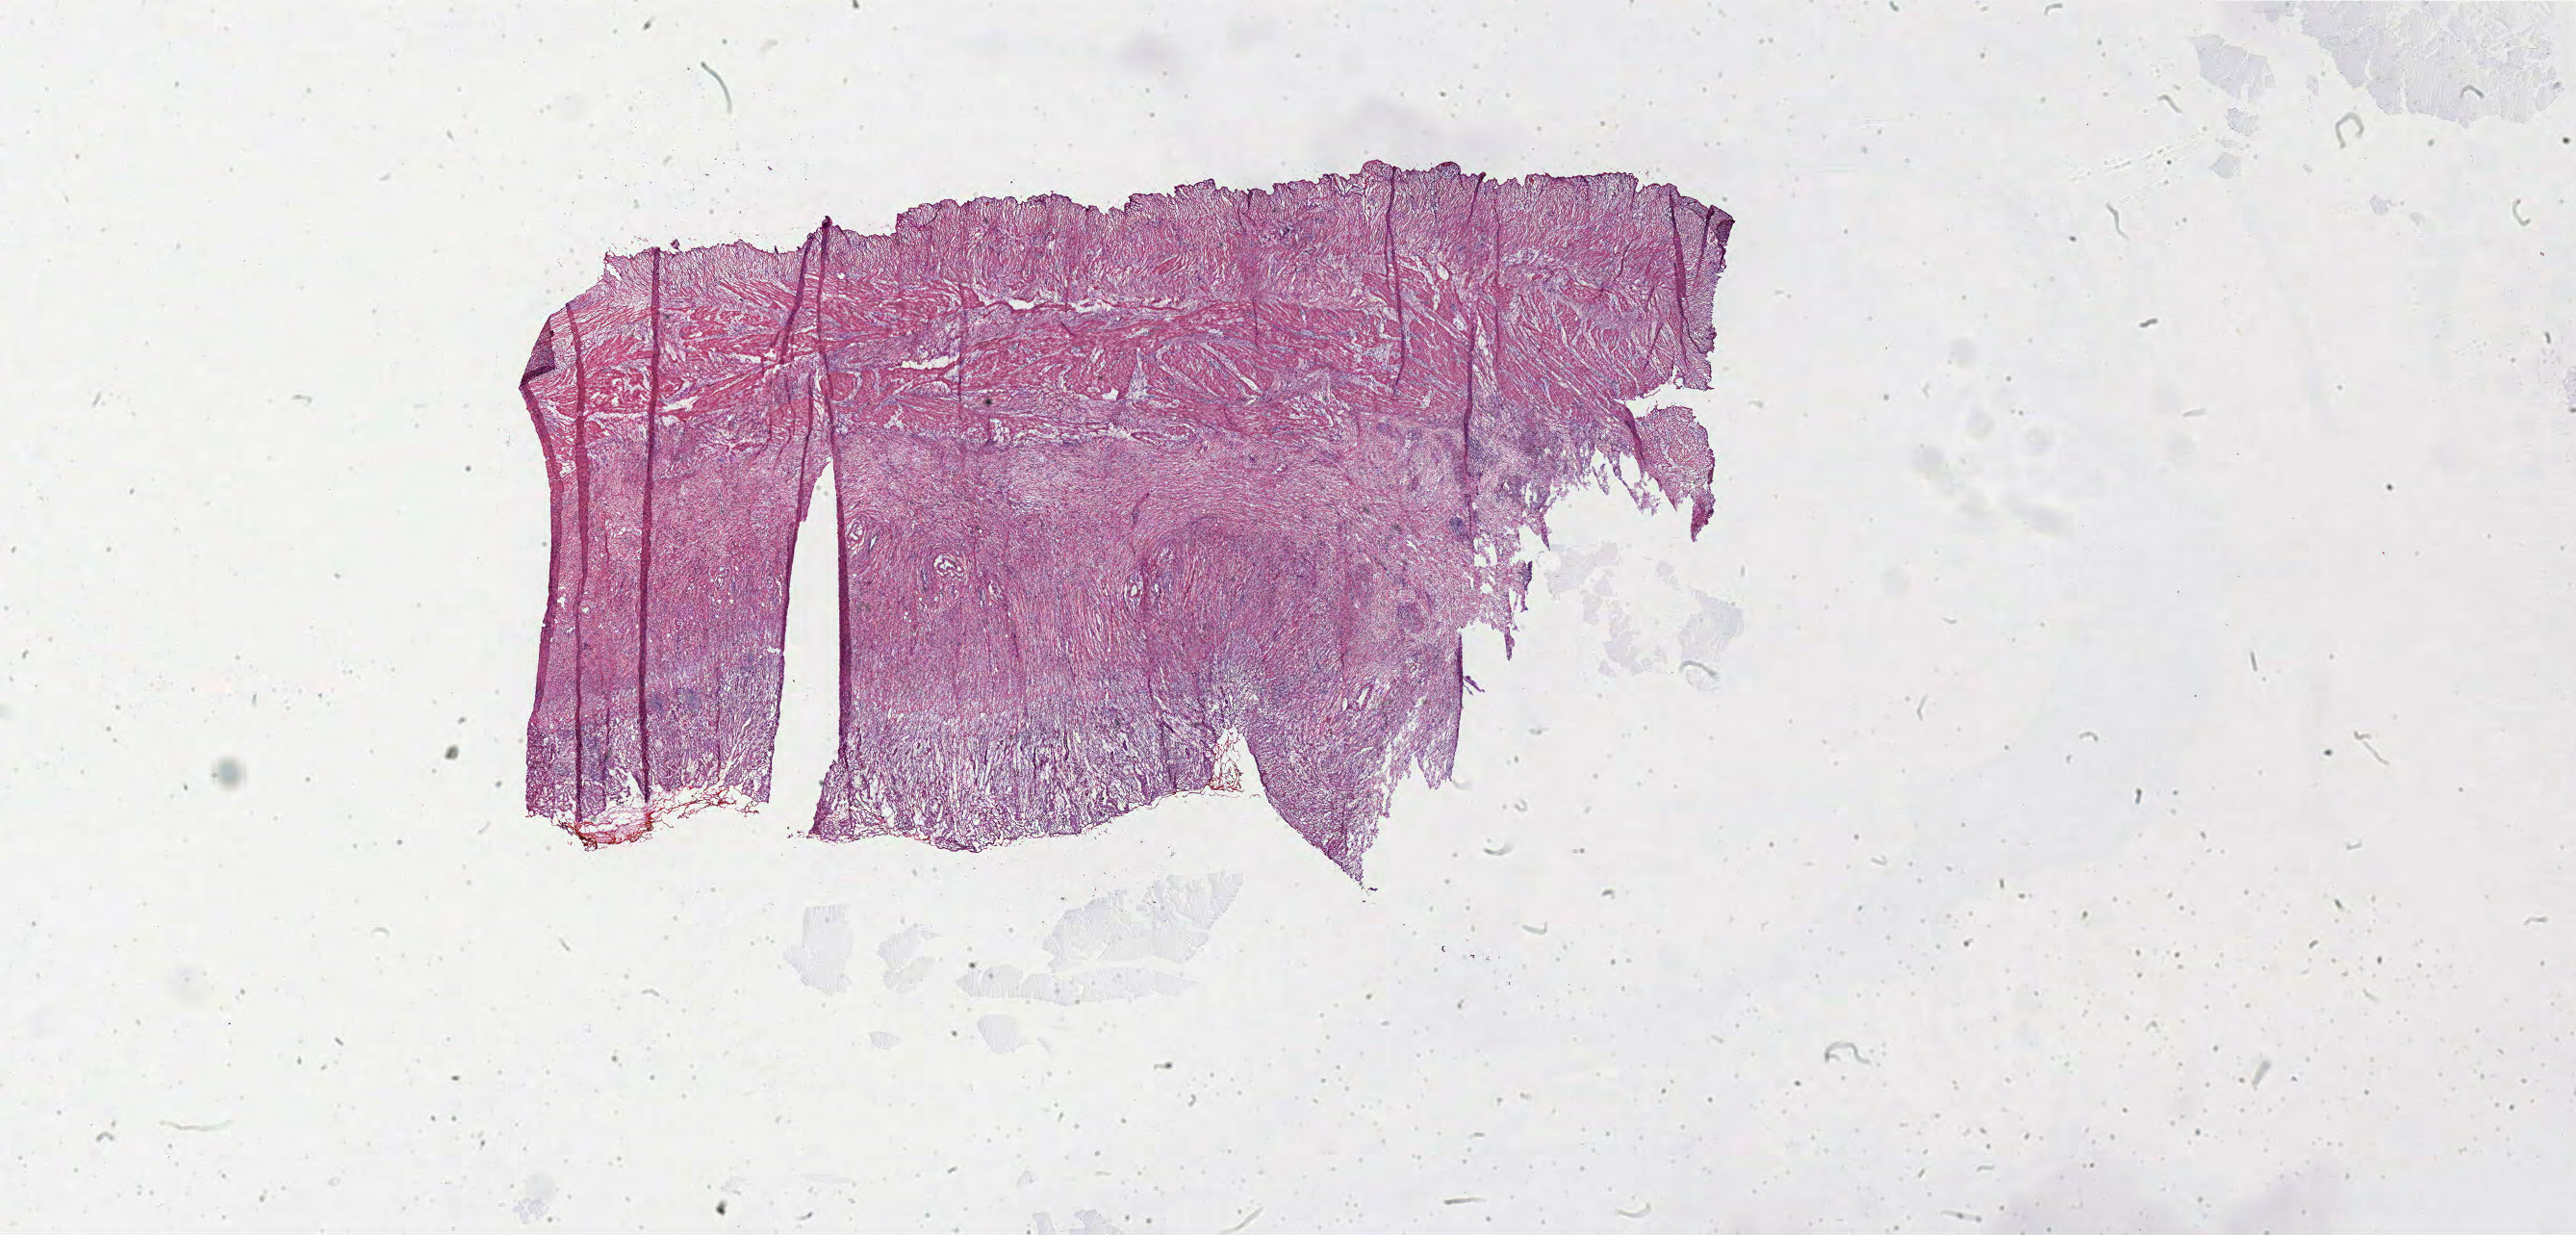
Hematoxylin and eosin (H&E) stained whole-slide image, a low-resolution overview of the entire scanned area, about 42.2 x 20.2 mm. Frozen section from the top of the tissue portion. Stomach, primary tumour sample. Female patient; age at initial diagnosis 46 years. Composition of this section per pathologist review: tumour cells 68%, tumour nuclei 75%.
Pathologic diagnosis: Adenocarcinoma, NOS (body of stomach).